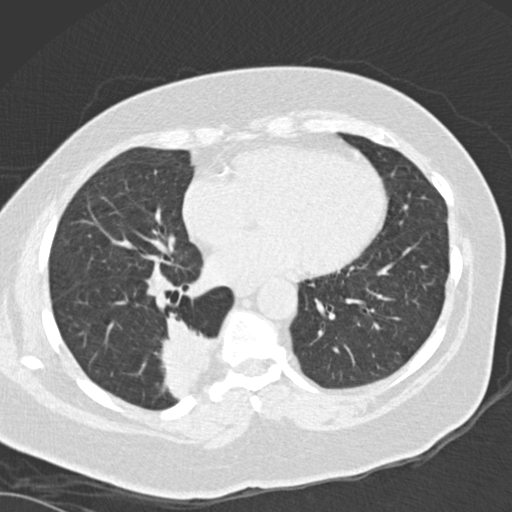
Axial slice from a low-dose chest CT screening exam, baseline screening round, lung window (W 1500 / L -600 HU), 2 mm slice thickness, 120 kVp. Female participant, aged 66 years at enrolment. Current smoker at enrolment.
Expert-annotated lung lesion, bounding box <149,319,229,401> (left, top, right, bottom; pixels). The screening reader recorded 3 non-calcified nodules or masses ≥4 mm on this exam; which of them this box marks is not recorded. Later outcome: lung cancer diagnosed 67 days after this screen — adenocarcinoma, NOS, right lower lobe, well differentiated (G1), stage IB (AJCC 6th edition), 55 mm at pathology.